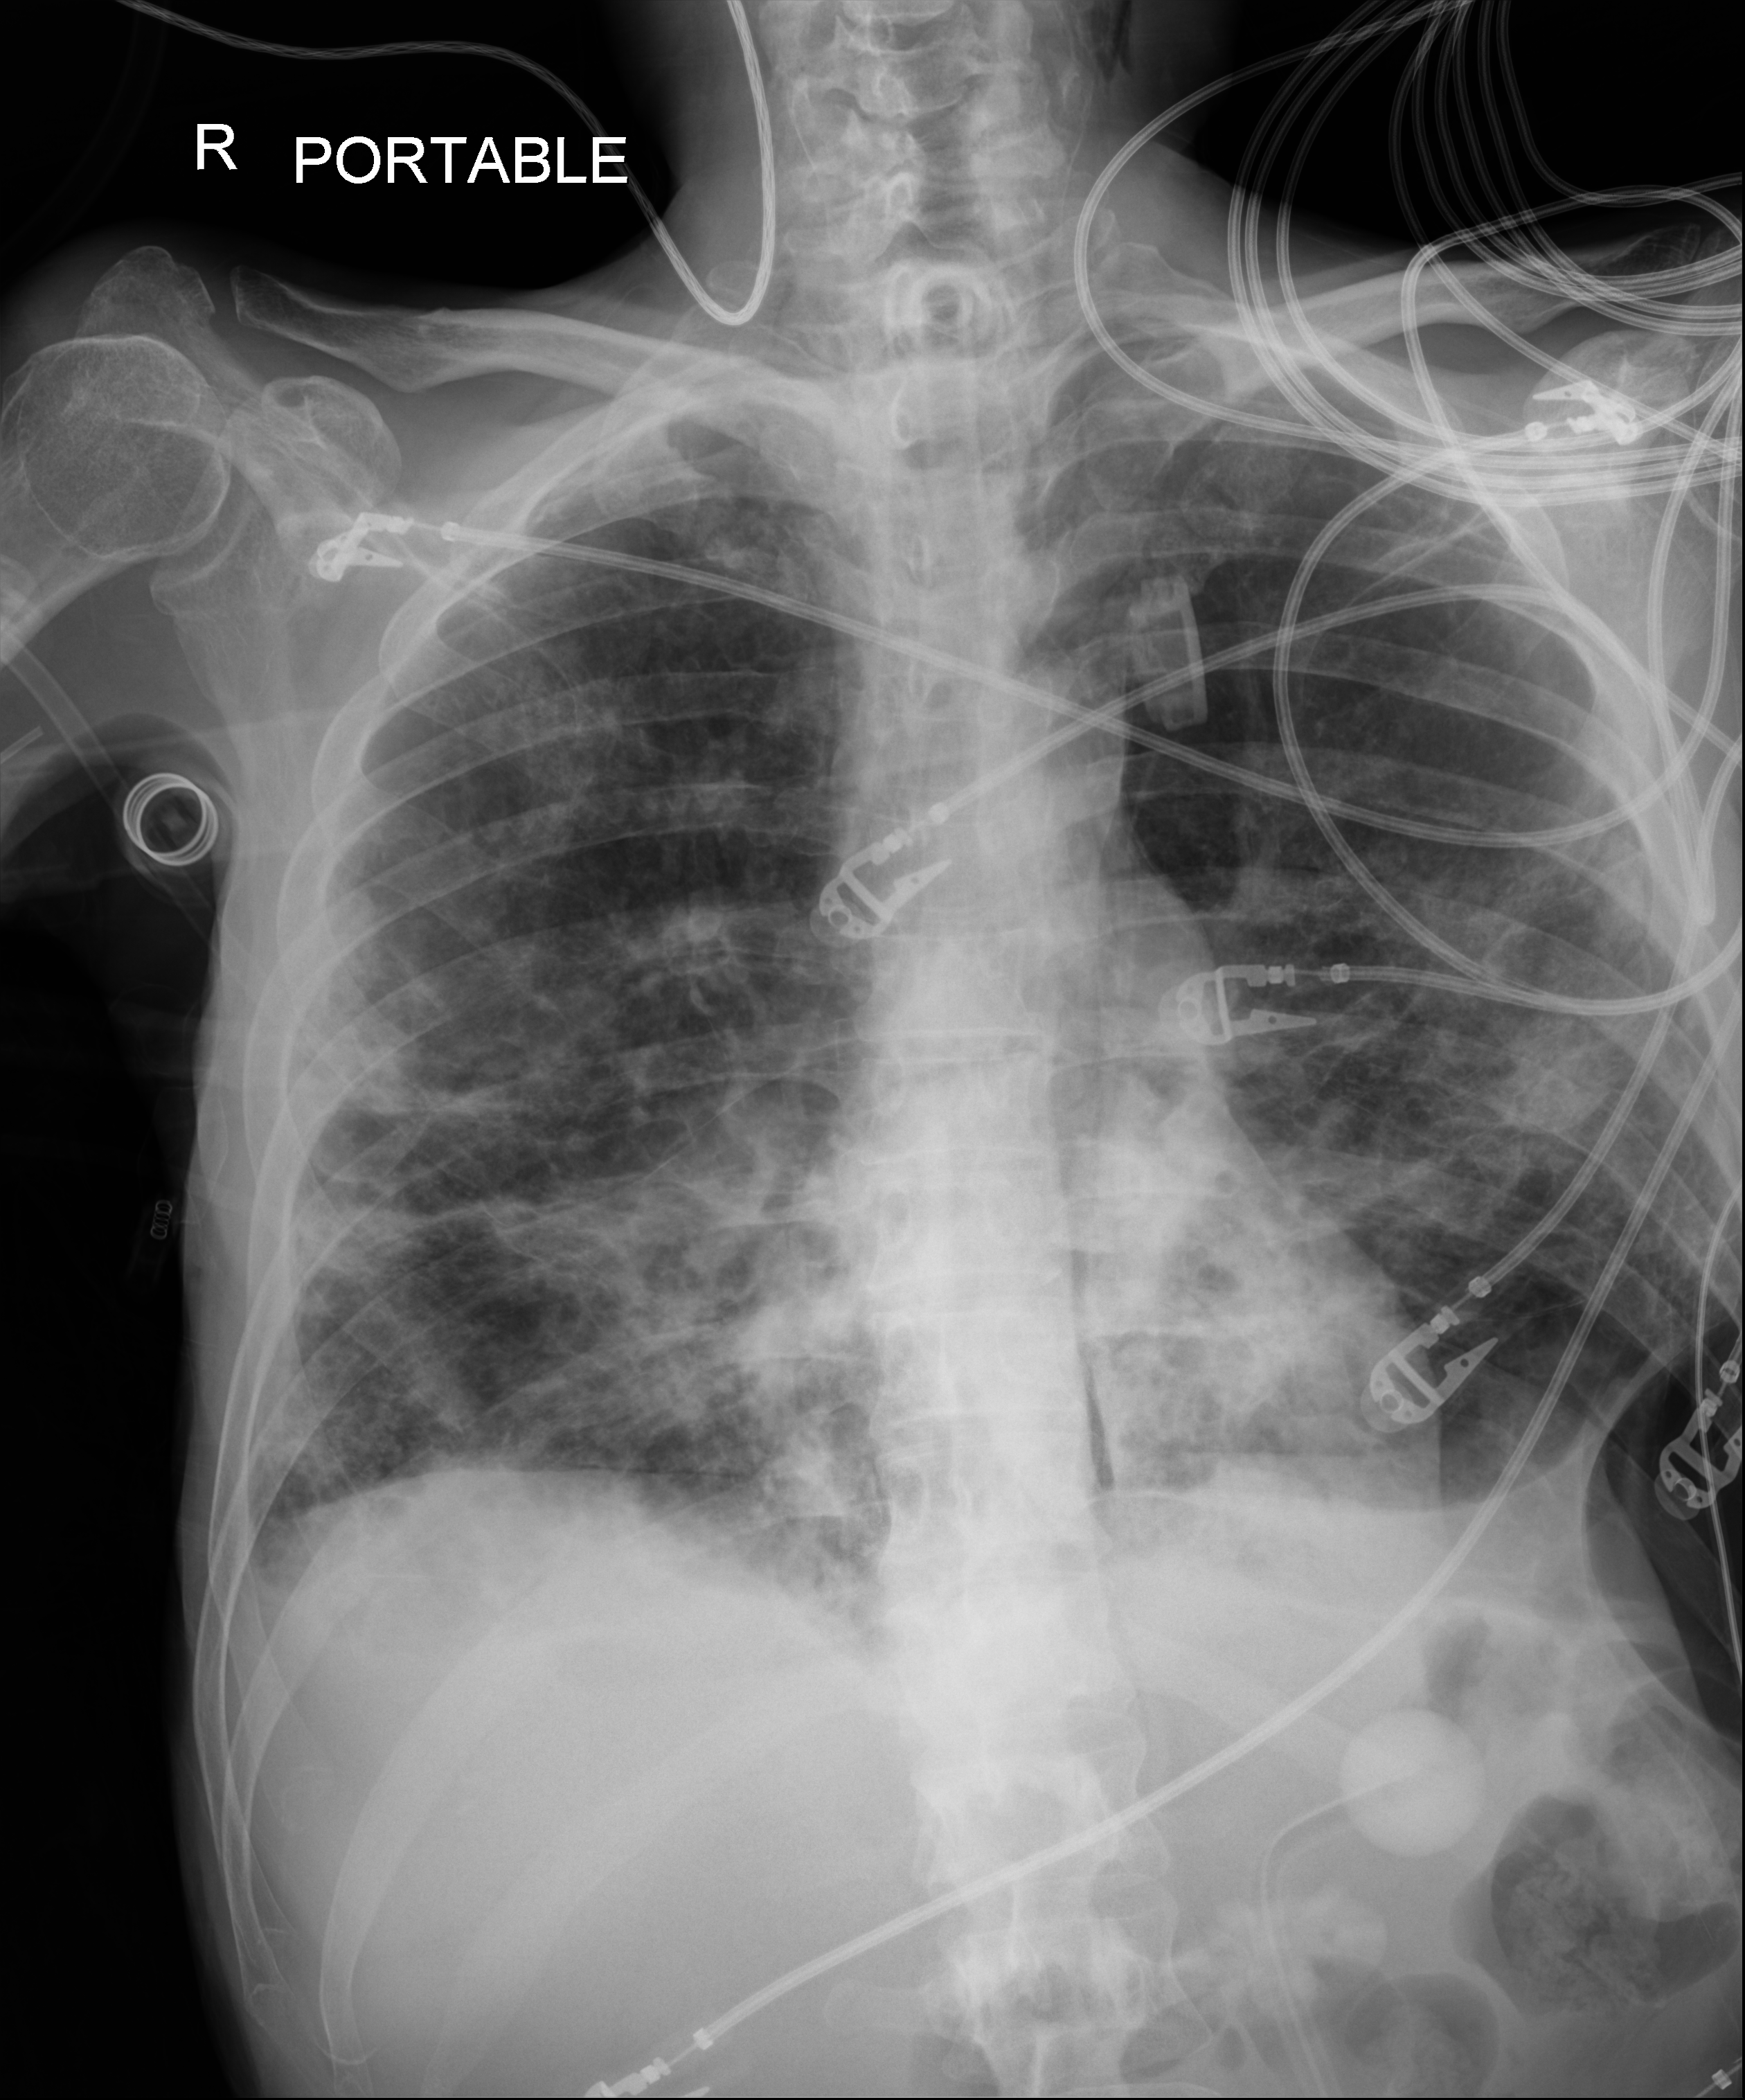
Chest radiograph, anteroposterior (AP) projection. Male patient hospitalised with COVID-19, age 18–59 years.
From the hospital-stay record, not from the radiograph (when in the stay this image was taken is not recorded): COPD (admission record): no.